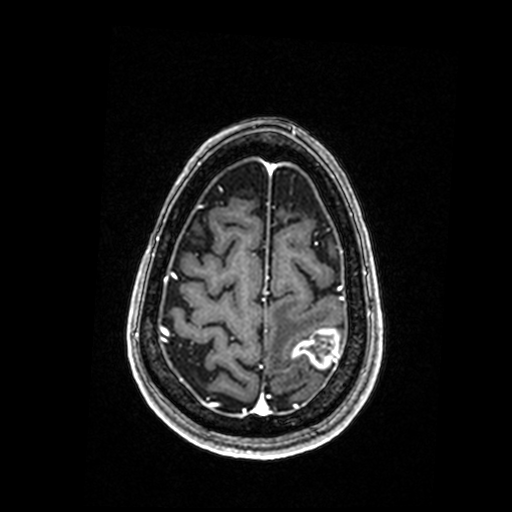
Brain MRI from a brain-tumour surgery series, one axial slice; T1-weighted post-contrast; 0.98 mm slice thickness; 512 × 512 image matrix, field of view 250 × 250 mm. Case-level facts recorded for this patient, not image findings: histopathology: Metastastic Carcinoma, Poorly Differentiated; tumour location: Left Parietal.
Annotated regions visible in this slice (manually delineated by an expert):
- tumour: bounding box <293,329,340,369> (left, top, right, bottom; pixels)